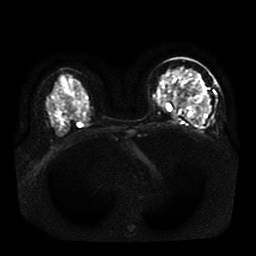
Breast MRI, one axial slice. Slice 25 of 41 in the series (ordered by position). Diffusion-weighted series; image 2 of 4 stored at this slice position (different b-values; order by instance number). 1.5 T. 256 × 256 image matrix, field of view 330 × 330 mm. Female patient.
Structures marked on this image (outlined manually by an expert reader):
- tumour on diffusion-weighted imaging: bounding box (x1, y1, x2, y2) in pixels: (188, 85, 209, 111)